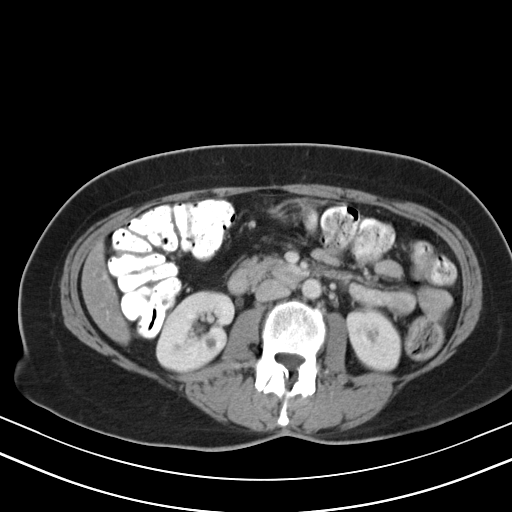
Contrast-enhanced abdominal CT, one axial slice; position 16 of 47 along the scan axis; reconstruction kernel B40s; soft-tissue window (W 400 / L 40 HU); 5 mm slice thickness; 512 × 512 image matrix, field of view 350 × 350 mm. Female patient. Case-level facts recorded for this patient, not image findings: diagnosis: colorectal cancer liver metastases, imaged before liver resection; multiple liver metastases: no; largest metastasis: 3.5 cm.
Outlined on this slice (manually delineated by an expert):
- liver: box from (x=84, y=249) to (x=126, y=340) px
- planned liver remnant (the part of the liver to remain after resection): (x=84, y=249)–(x=126, y=339)